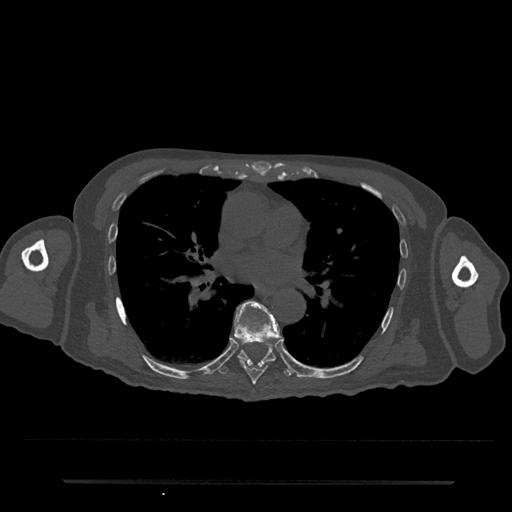
CT including the spine, one axial slice; position 455 of 797 along the scan axis; bone window (W 1800 / L 400 HU); 0.5 mm slice thickness; 512 × 512 image matrix, field of view 427 × 427 mm. Patient: male, 74 years. Case-level facts recorded for this patient, not image findings: primary cancer: prostate.
Outlined on this slice (semi-automatic segmentation, software-assisted and operator-edited):
- T7 vertebra: box from (x=234, y=301) to (x=283, y=385) px
- T8 vertebra: (x=219, y=342)–(x=292, y=377)